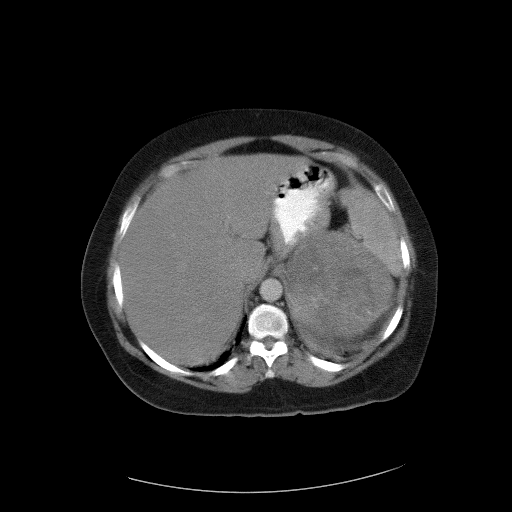
Contrast-enhanced abdominal CT, one axial slice. Position 78 of 90 along the scan axis. Intravenous contrast given. Soft-tissue window (W 400 / L 40 HU). 5 mm slice thickness. 512 × 512 image matrix, field of view 480 × 480 mm. Patient: female, 55 years. Case-level facts recorded for this patient, not image findings: diagnosis: adrenocortical carcinoma; tumour side: left adrenal; tumour size at pathology: 22 cm; Ki-67 index: 10 %; stage (as recorded): 3.
Outlined on this slice (semi-automatically segmented with operator editing):
- mass: bounding box [x1, y1, x2, y2] px = [291, 233, 391, 338]